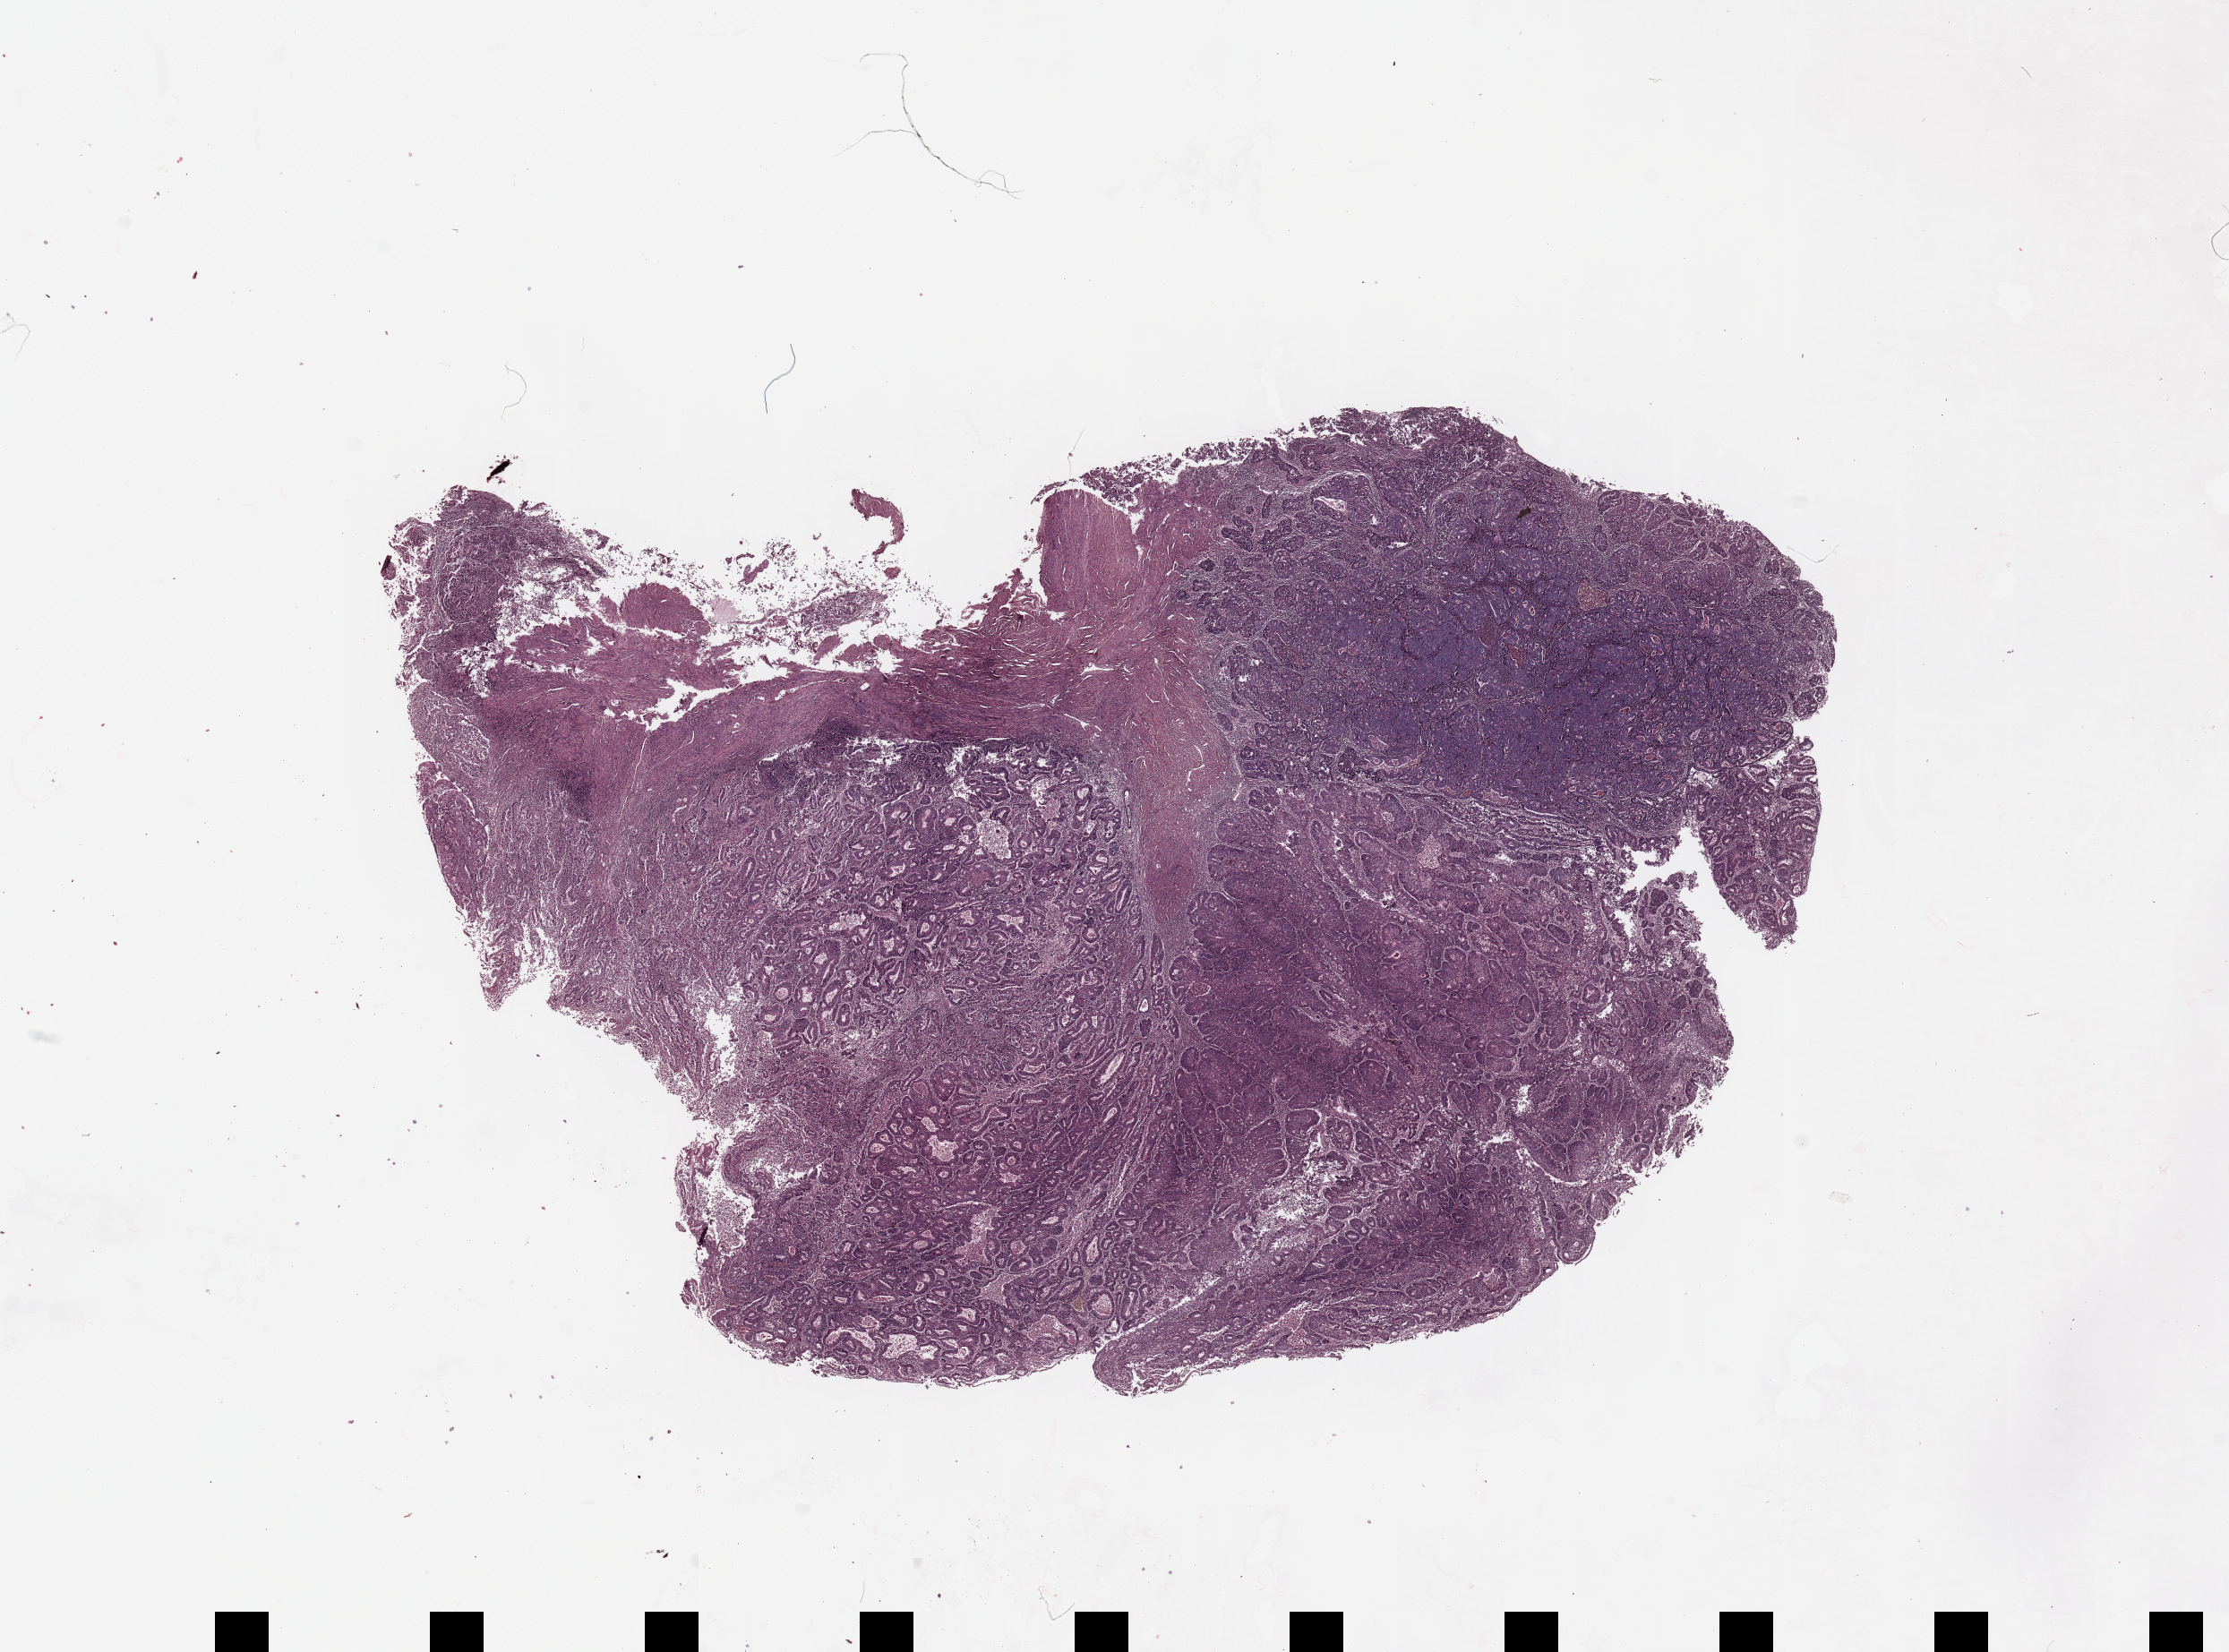
Whole-slide histology image, H&E — whole scanned area (about 19.7 x 14.6 mm, acquisition: 20x scan) shown as a low-resolution overview. Tumour tissue sample, uterus. Female, 69 y/o. Histologic grade: G2 (moderately differentiated).
AJCC pathologic stage: I. Histologic diagnosis: Endometrioid adenocarcinoma, NOS.